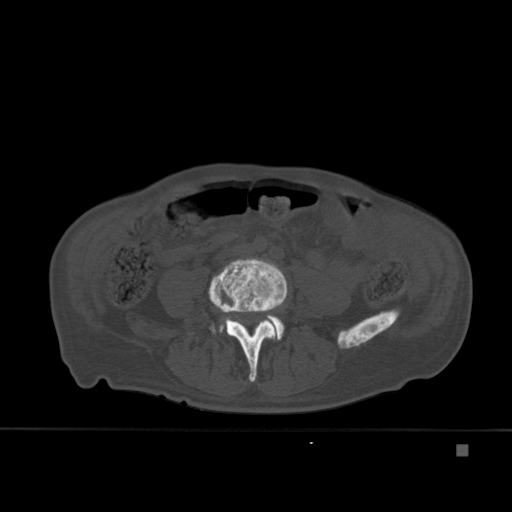
CT including the spine, one axial slice; position 118 of 451 along the scan axis; bone window (W 1800 / L 400 HU); 1.5 mm slice thickness; 512 × 512 image matrix, field of view 378 × 378 mm. Male patient, age 75 years. From the clinical record (not read from this slice): primary cancer: prostate.
Structures marked on this image (semi-automatic segmentation, software-assisted and operator-edited):
- L4 vertebra: bounding box [x1, y1, x2, y2] px = [208, 258, 288, 382]
- L5 vertebra: [220, 314, 285, 341]
- T7 vertebra: [219, 315, 275, 332]